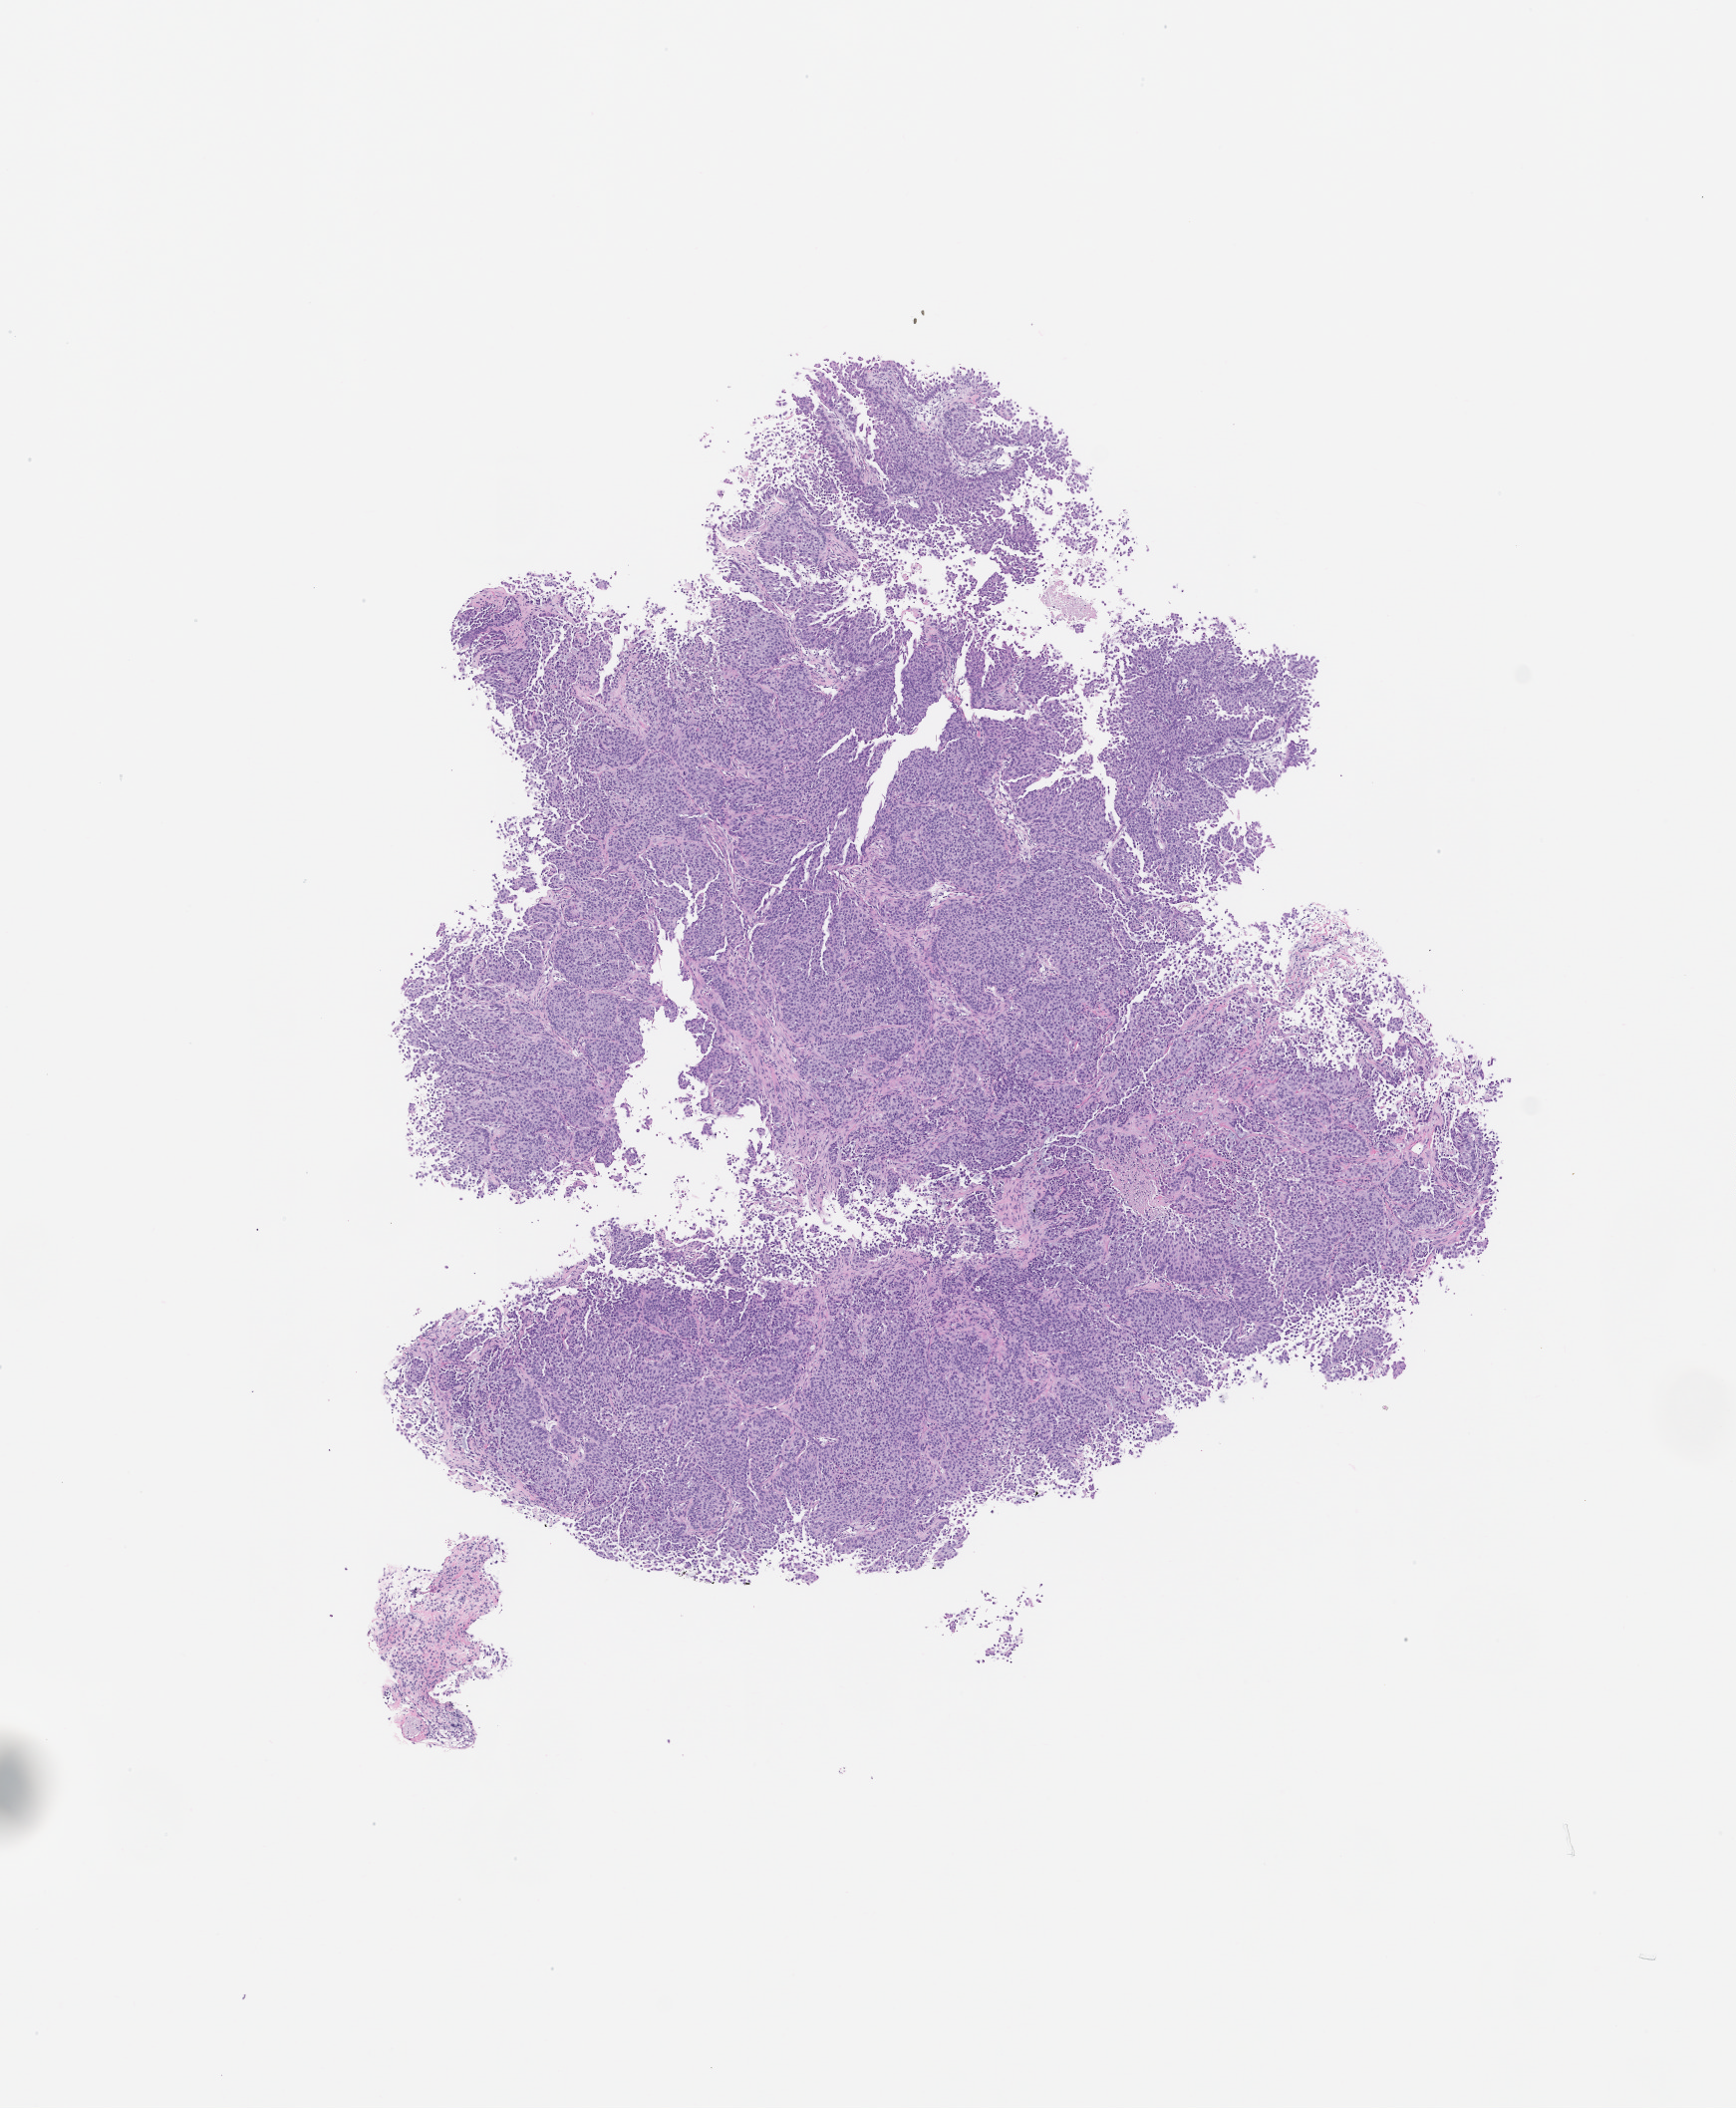
H&E whole-slide image of a patient-derived xenograft (PDX) tumor grown in a mouse, passage 2, whole scanned area (about 7.0 x 8.5 mm) shown as a low-resolution overview, formalin-fixed, paraffin-embedded (FFPE) tissue, tumor site category: bladder.
Originating patient diagnosis: Urothelial Carcinoma.